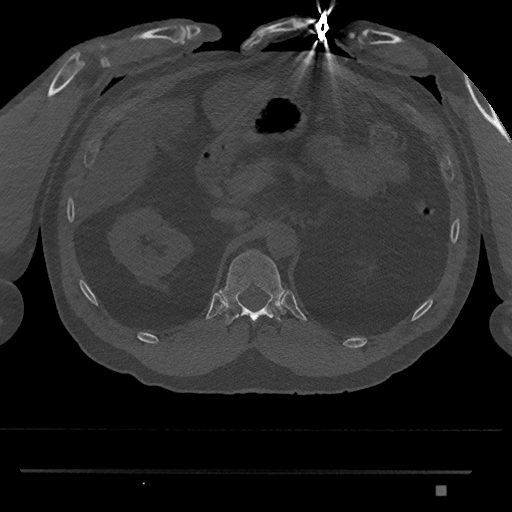
CT including the spine, one axial slice; position 890 of 1134 along the scan axis; 120 kVp; bone window (W 1800 / L 400 HU); 0.5 mm slice thickness; 512 × 512 image matrix, field of view 429 × 429 mm. Patient: male, 65 years. From the clinical record (not read from this slice): primary cancer: prostate.
Outlined on this slice (semi-automatically segmented with operator editing):
- T12 vertebra: bounding box (x1, y1, x2, y2) in pixels: (219, 250, 287, 325)